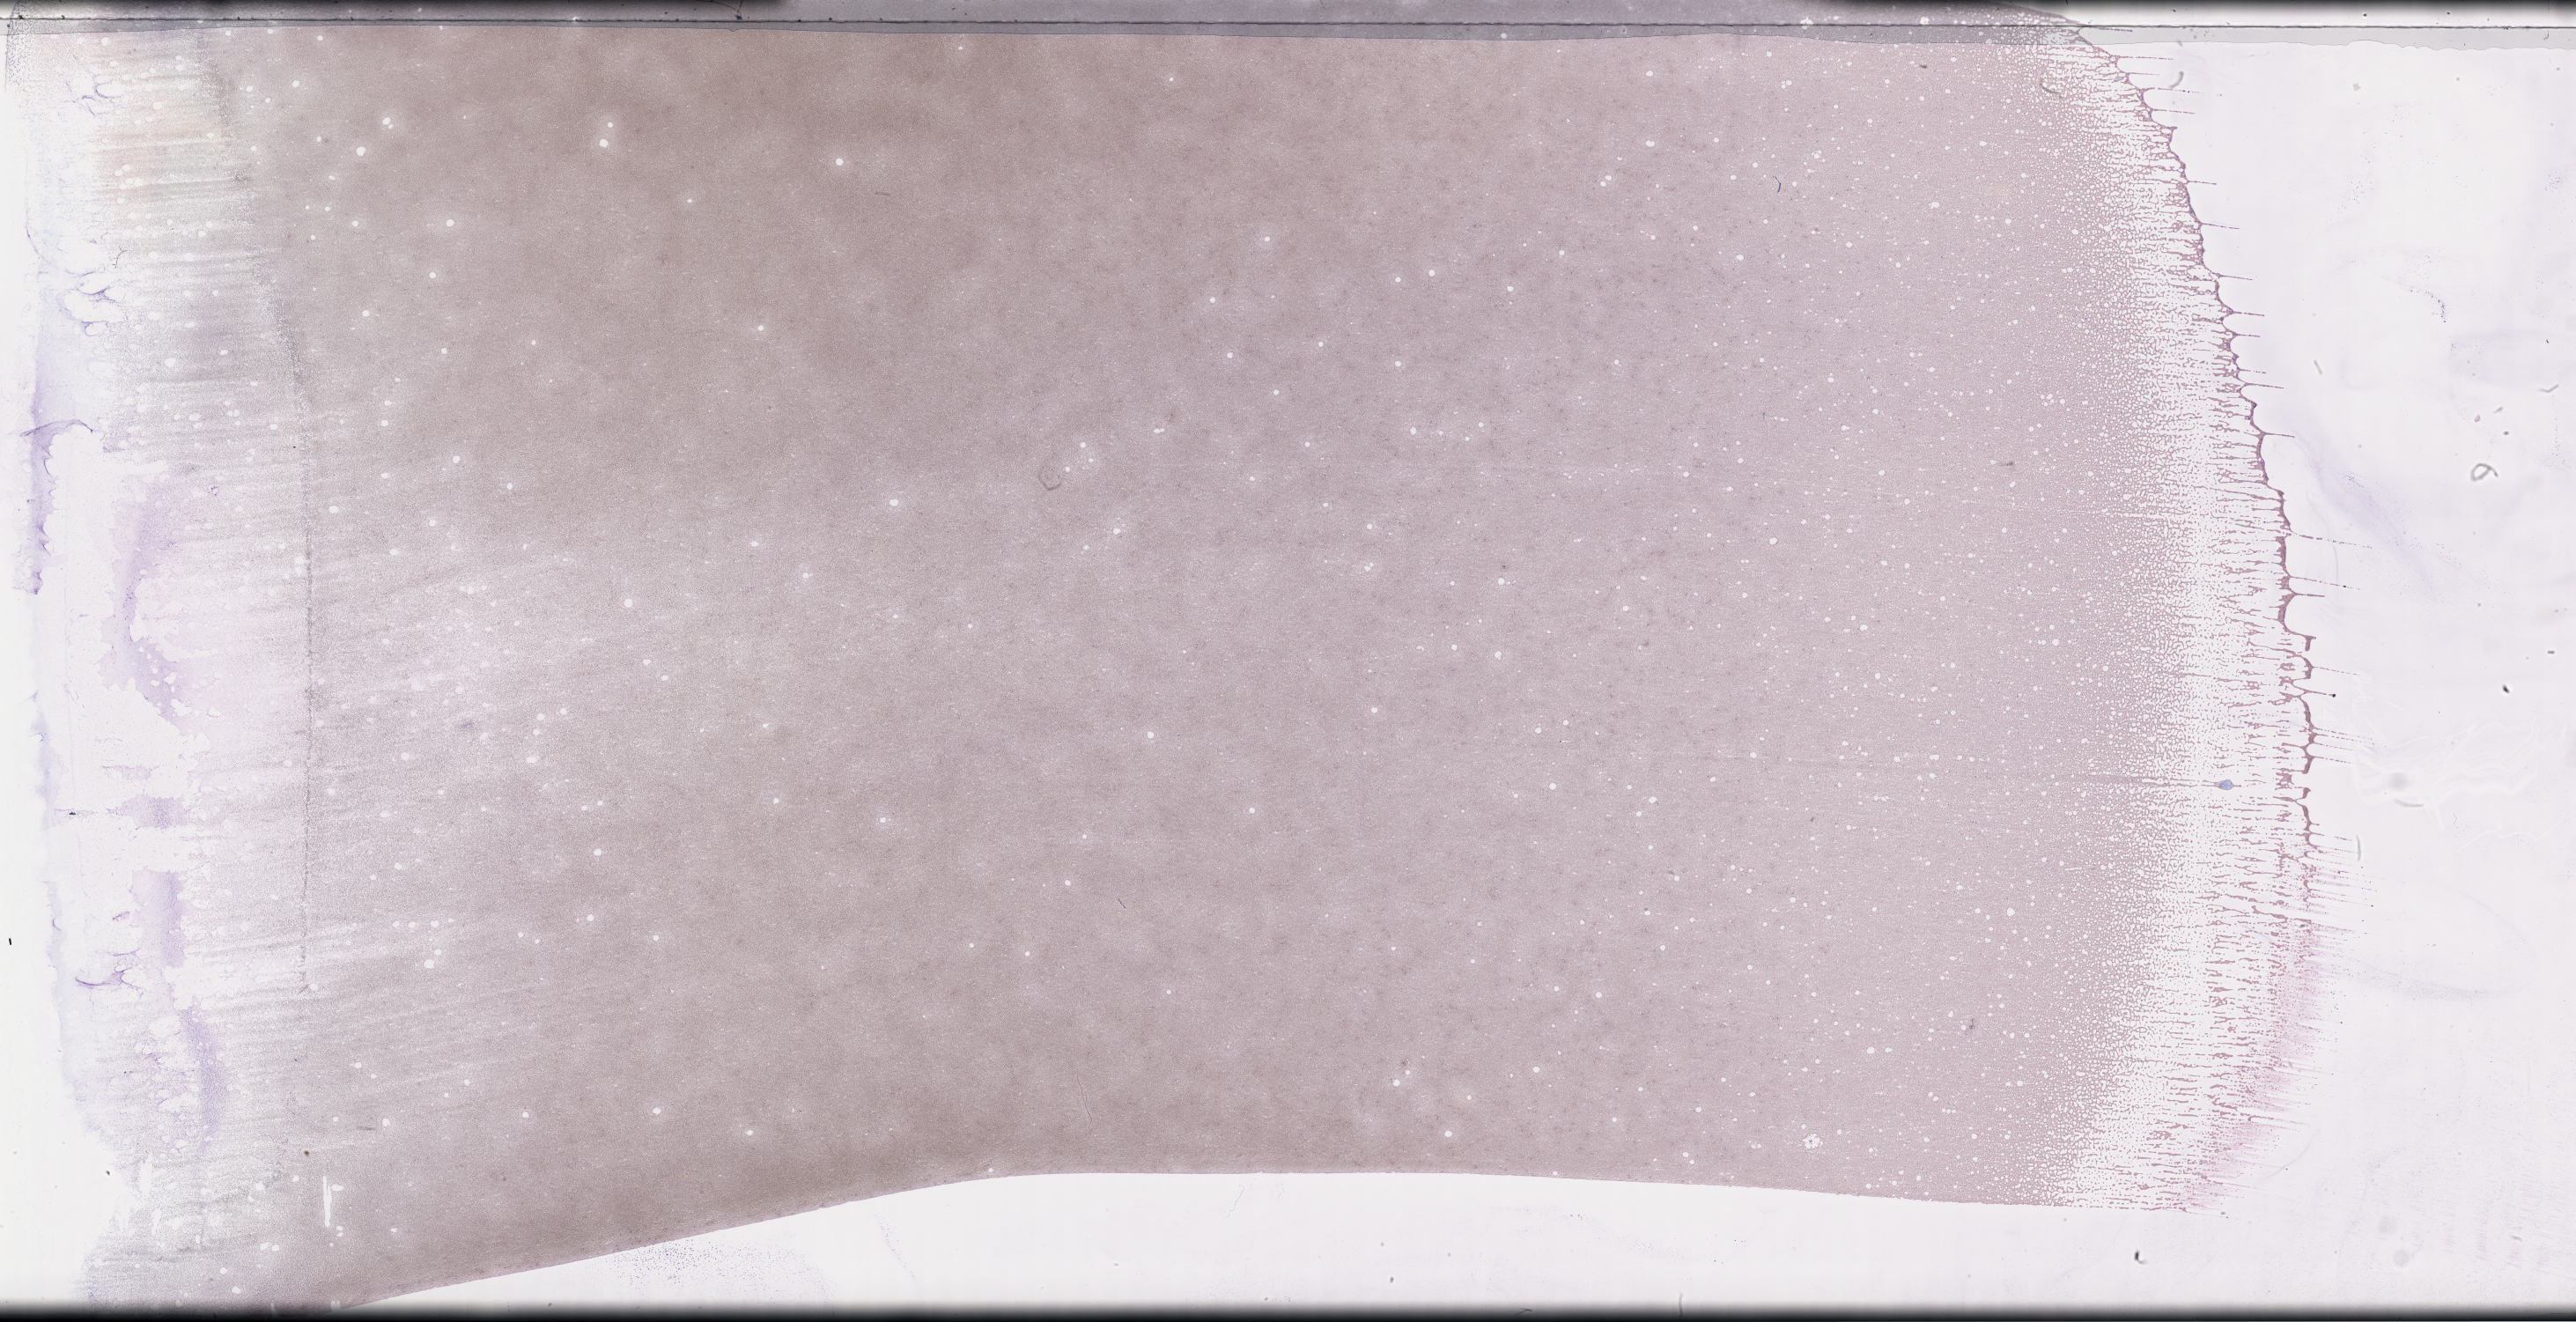
Wright-Giemsa-stained whole blood smear, whole-slide image — shown as a low-resolution overview of the whole scanned area (about 47.2 x 24.2 mm); smear from an EDTA sample; specimen time point: collected on treatment. Female patient.
From a patient with: Plasma Cell Myeloma.